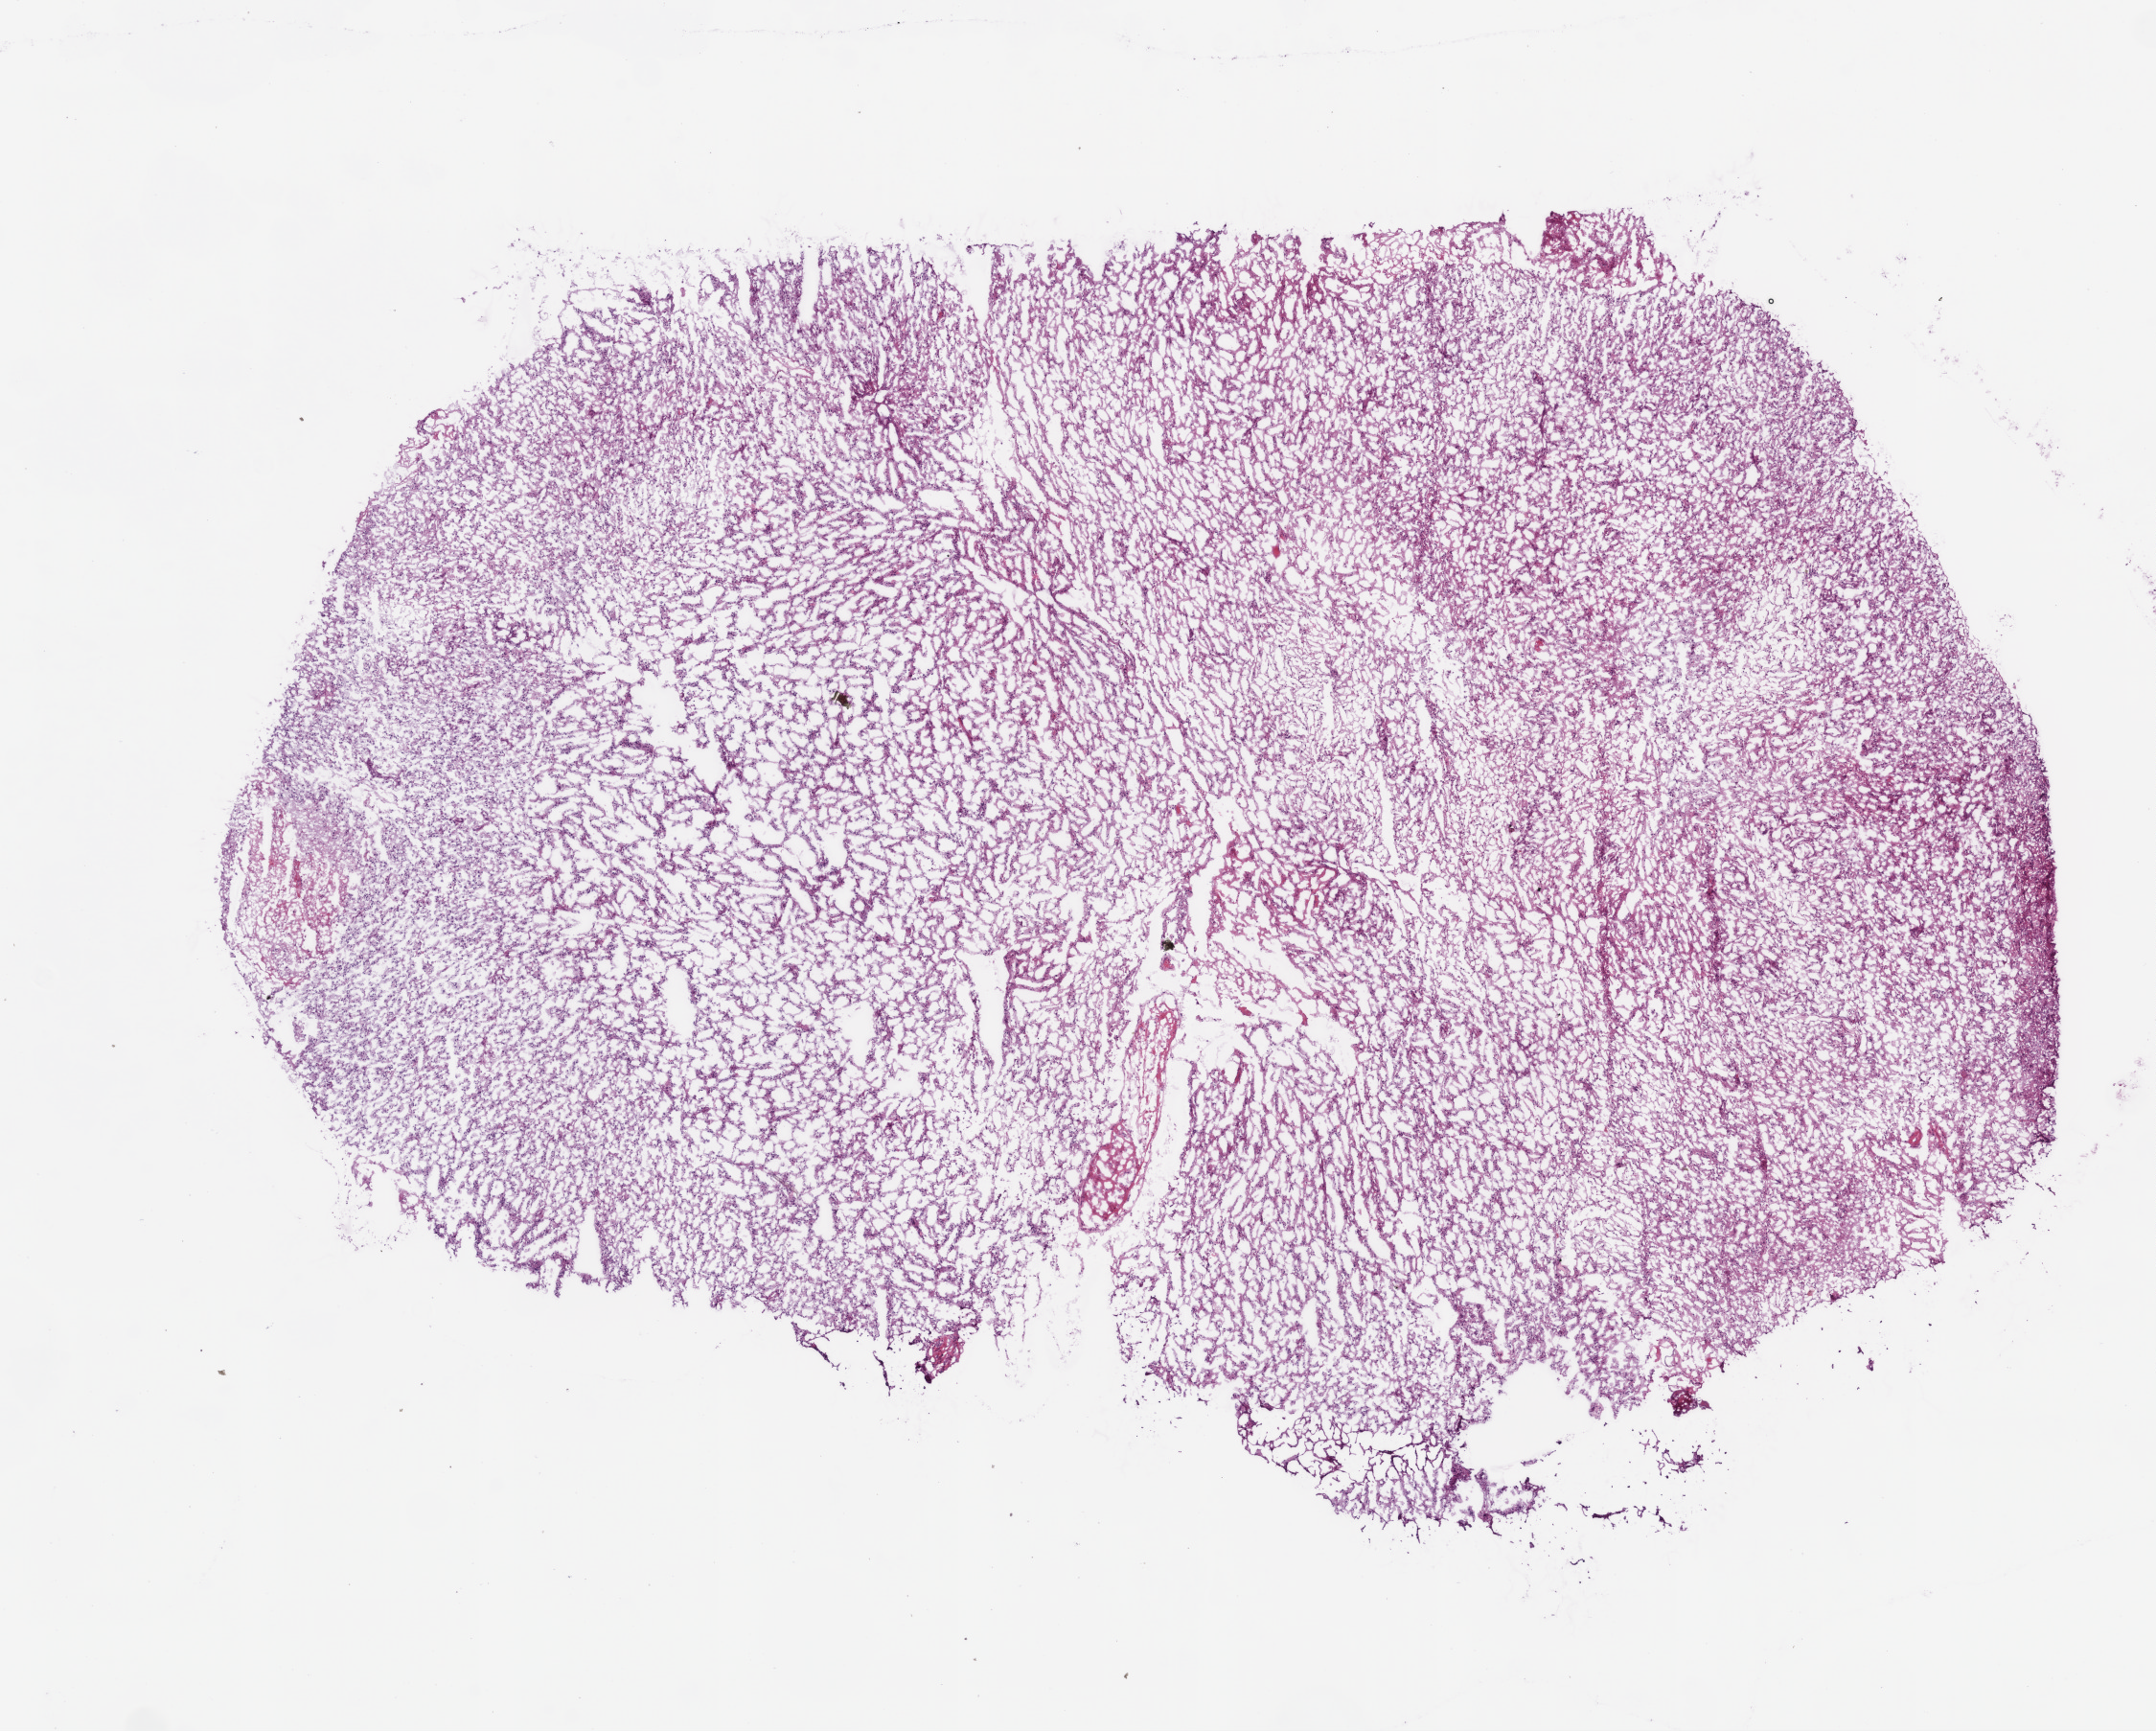
Digitized Hematoxylin and eosin (H&E) stained tissue section (whole slide) — shown as a low-resolution overview of the whole scanned area (about 9.0 x 7.2 mm); frozen section from the bottom of the tissue portion; sample: primary tumour, brain. Female patient; age at initial diagnosis 72 years. Pathologist review of this section (percent, as recorded): tumour nuclei 80%, normal cells 0%, stromal cells 0%, necrosis 0%.
Diagnosis: Glioblastoma.